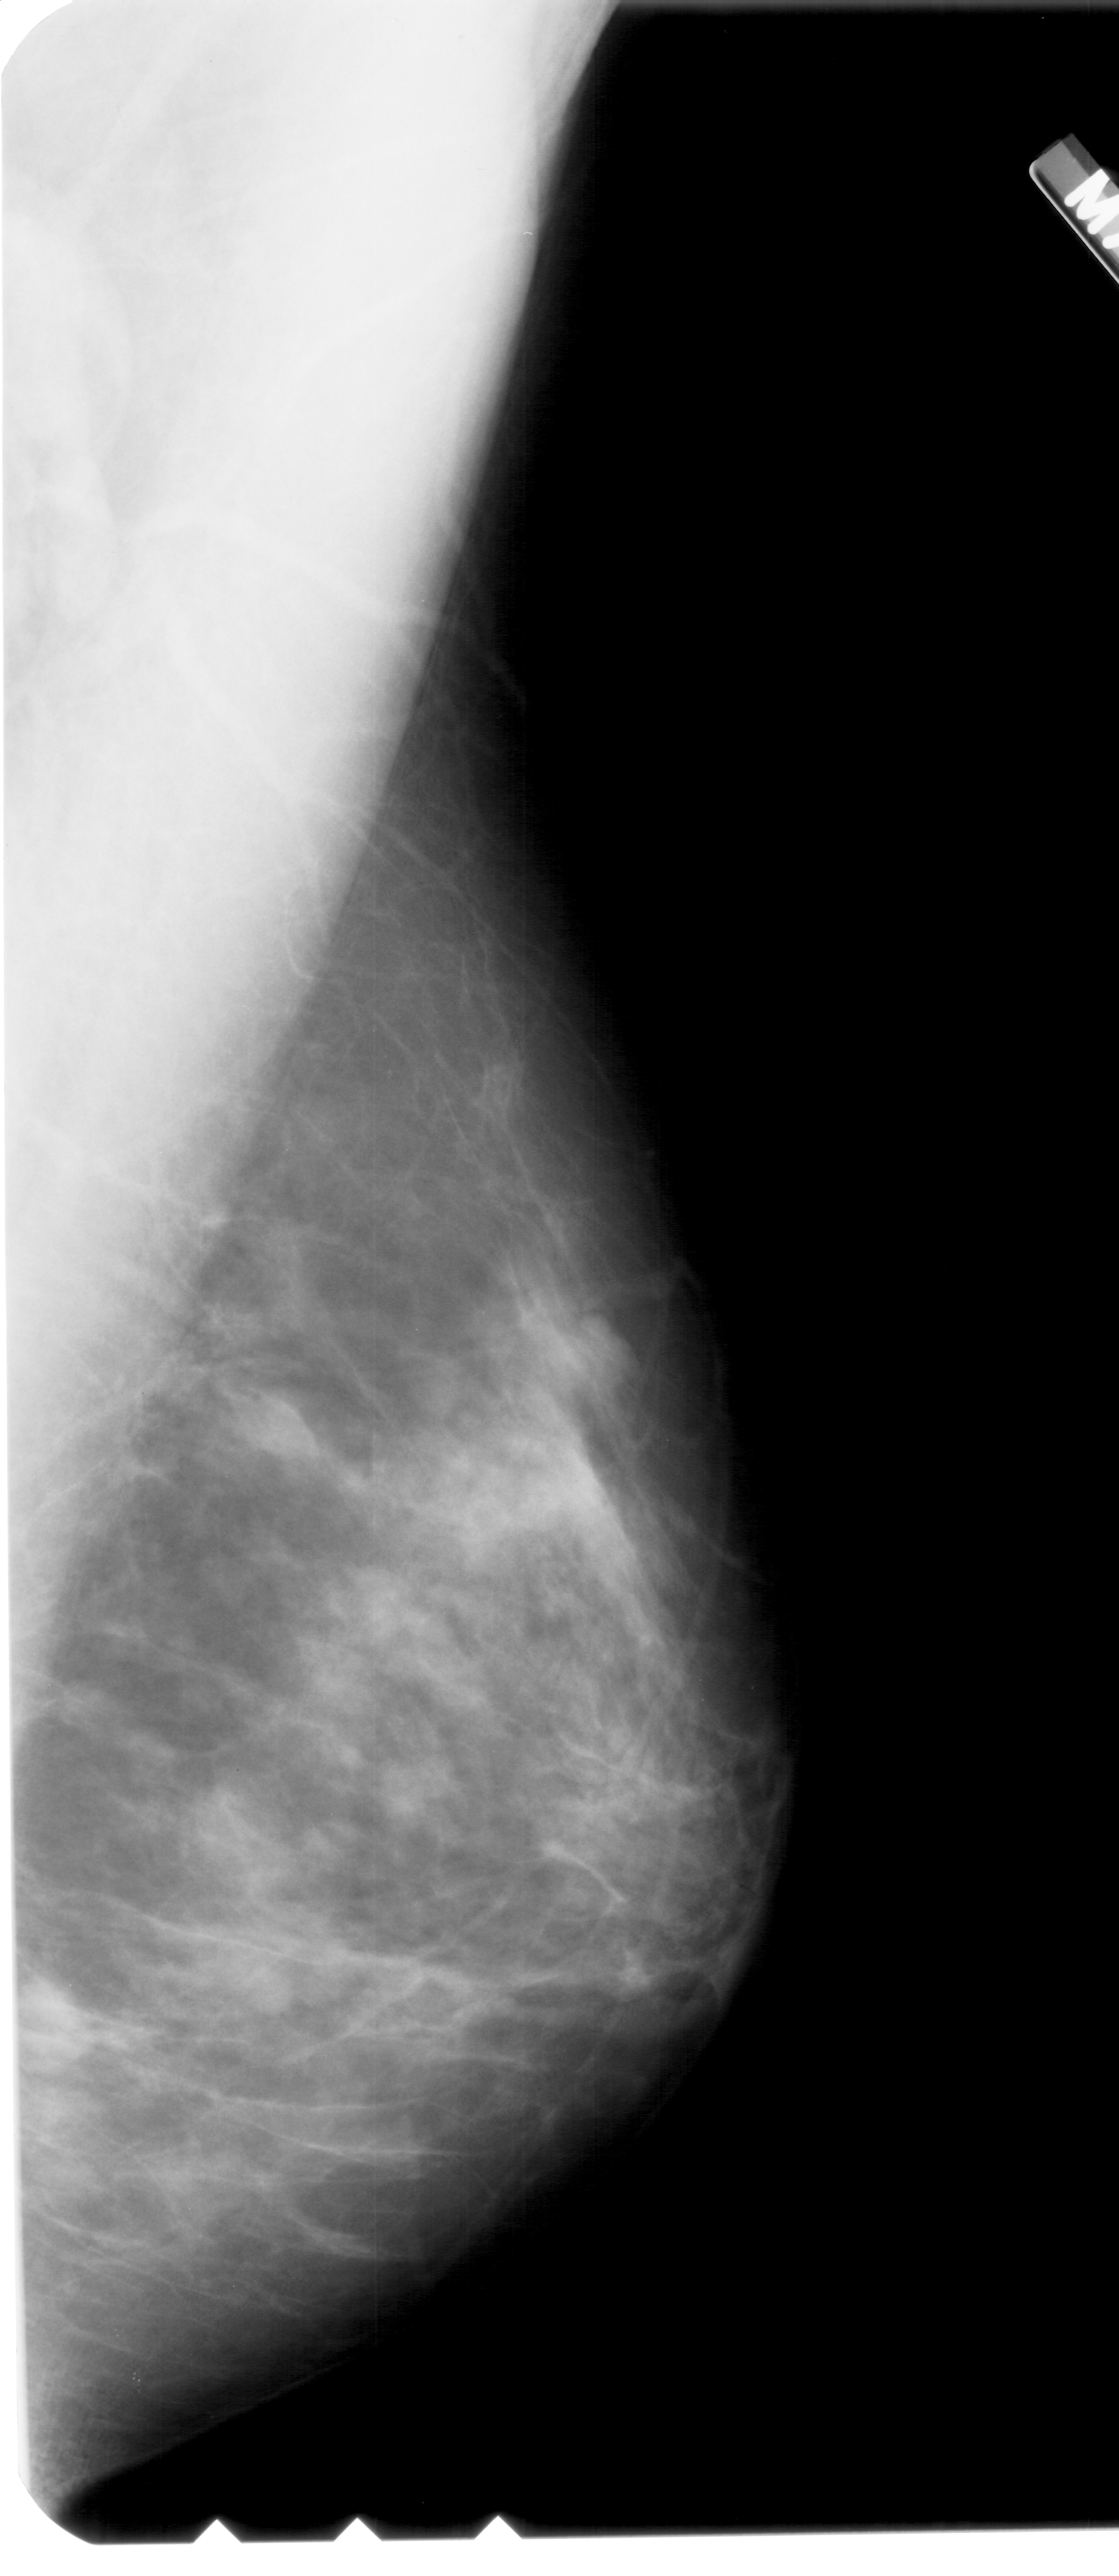
Scanned film-screen mammogram; right breast; mediolateral oblique (MLO) view; 1119 × 2576 image matrix.
Marked abnormalities (boxes around the expert regions of interest):
- mass, shape lobulated, margins obscured; BI-RADS assessment category 3; pathology (as recorded): benign: bounding box <31,1976,120,2060> (left, top, right, bottom; pixels)